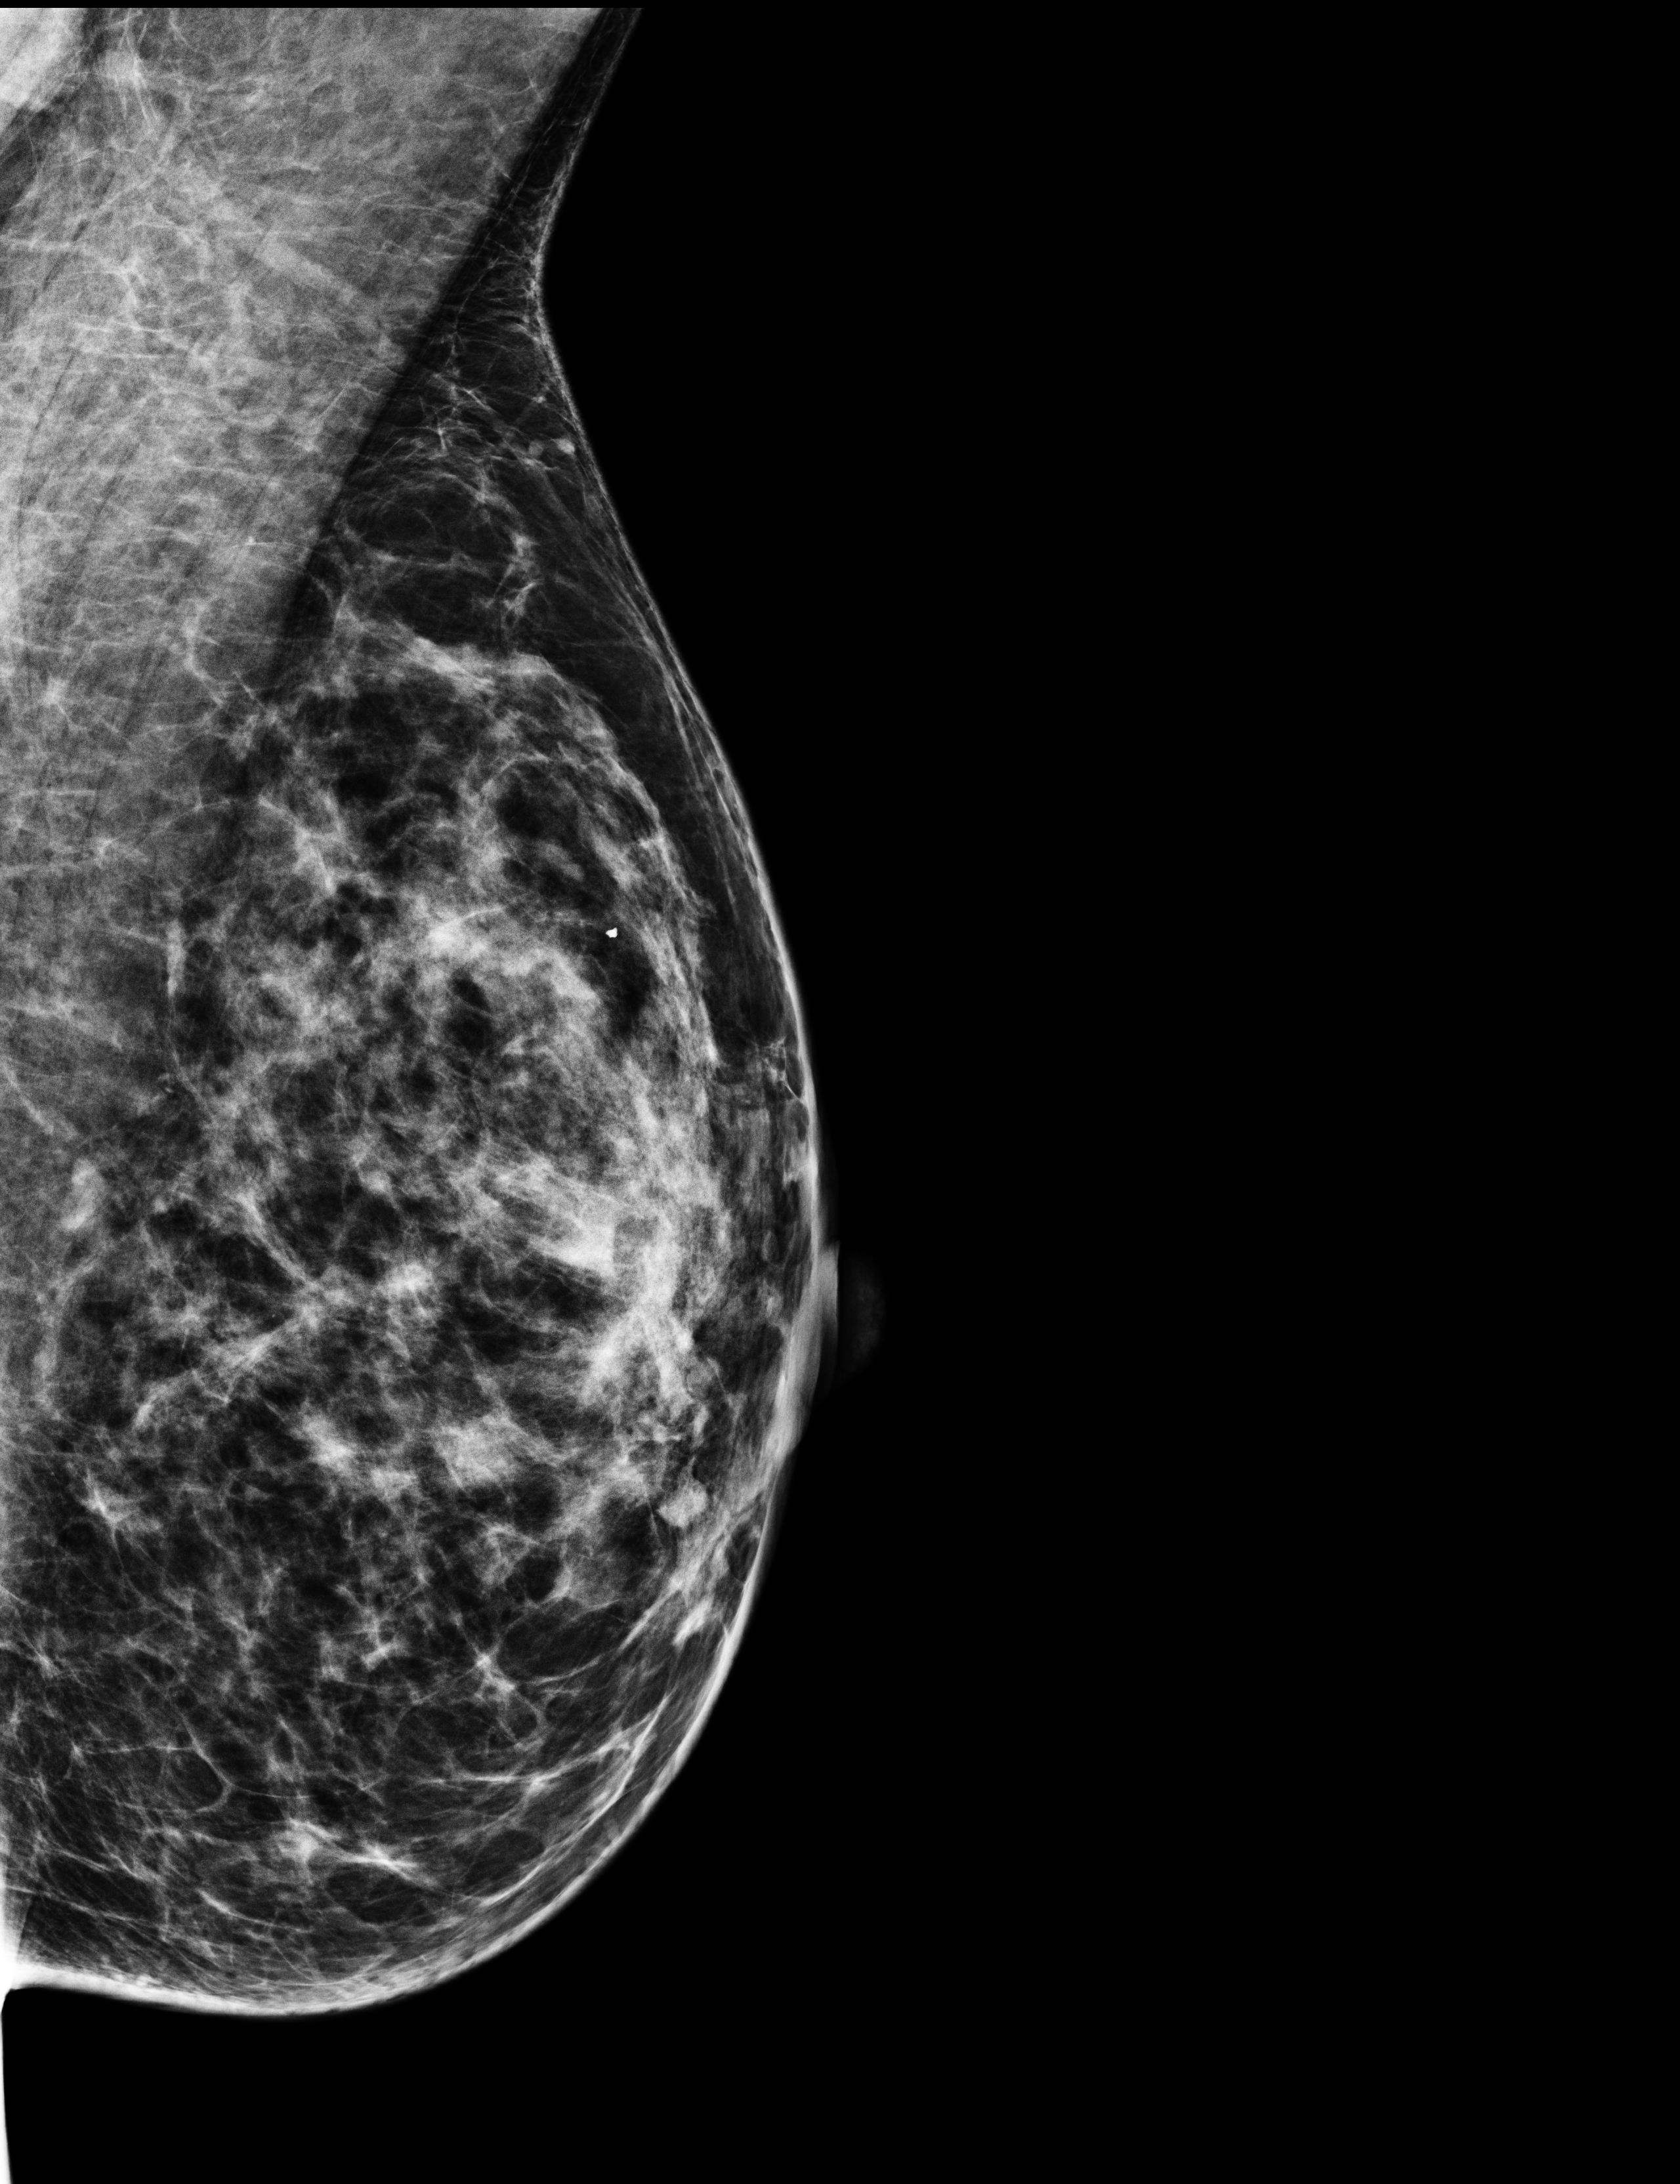
Screening examination; compressed breast thickness 59 mm; system: Selenia Dimensions. Patient aged 44 years (female).
Image type: full-field digital mammogram. Breast: left. Projection: mediolateral oblique (MLO) view.